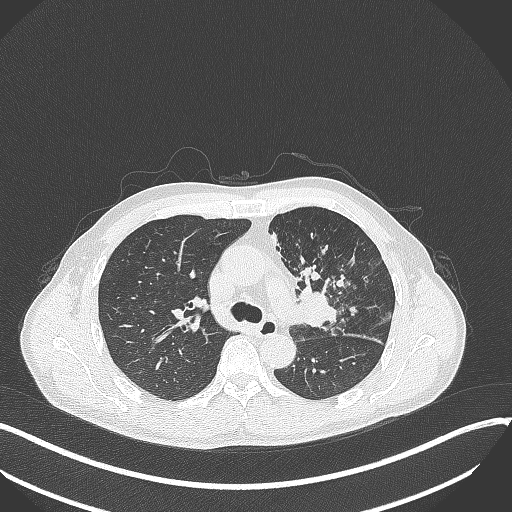
Chest CT, one axial slice; position 225 of 411 along the scan axis; reconstruction kernel B70f; lung window (W 1500 / L -600 HU); 1 mm slice thickness; 512 × 512 image matrix. Male patient, age 56 years. From the clinical record (not read from this slice): clinical TNM (as recorded): T2a N0 M0.
Outlined on this slice (rectangle marked by the reading radiologist):
- lung tumour (recorded histology: squamous cell carcinoma): box from (x=298, y=277) to (x=341, y=328) px